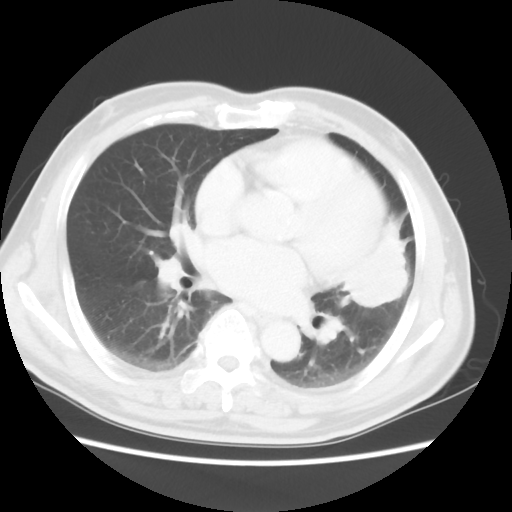
Chest CT, one axial slice; slice 23 of 50 in the series (ordered by position); 120 kVp; lung window (W 1500 / L -600 HU); 5 mm slice thickness; 512 × 512 image matrix, field of view 360 × 360 mm. Male patient, age 69 years. Case-level facts recorded for this patient, not image findings: clinical TNM (as recorded): T3 N1 M1a.
Outlined on this slice (rectangle marked by the reading radiologist):
- lung tumour (recorded histology: squamous cell carcinoma): bounding box (x1, y1, x2, y2) in pixels: (343, 216, 434, 321)